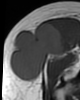
MRI of an extremity soft-tissue mass, one axial slice; slice 24 of 46 in the series (ordered by position); MR volume resampled by the dataset authors to the PET/CT grid (not the native acquisition matrix); 3.27 mm slice thickness; 80 × 100 image matrix. Female patient. From the clinical record (not read from this slice): histological type: synovial sarcoma; grade: intermediate; site of the primary tumour: right thigh.
Annotated regions visible in this slice (expert contour drawn on MRI and transferred to this co-registered scan by the dataset authors):
- gross tumour volume including surrounding oedema: box from (x=10, y=21) to (x=65, y=82) px
- gross tumour volume (mass): (x=10, y=21)–(x=65, y=82)